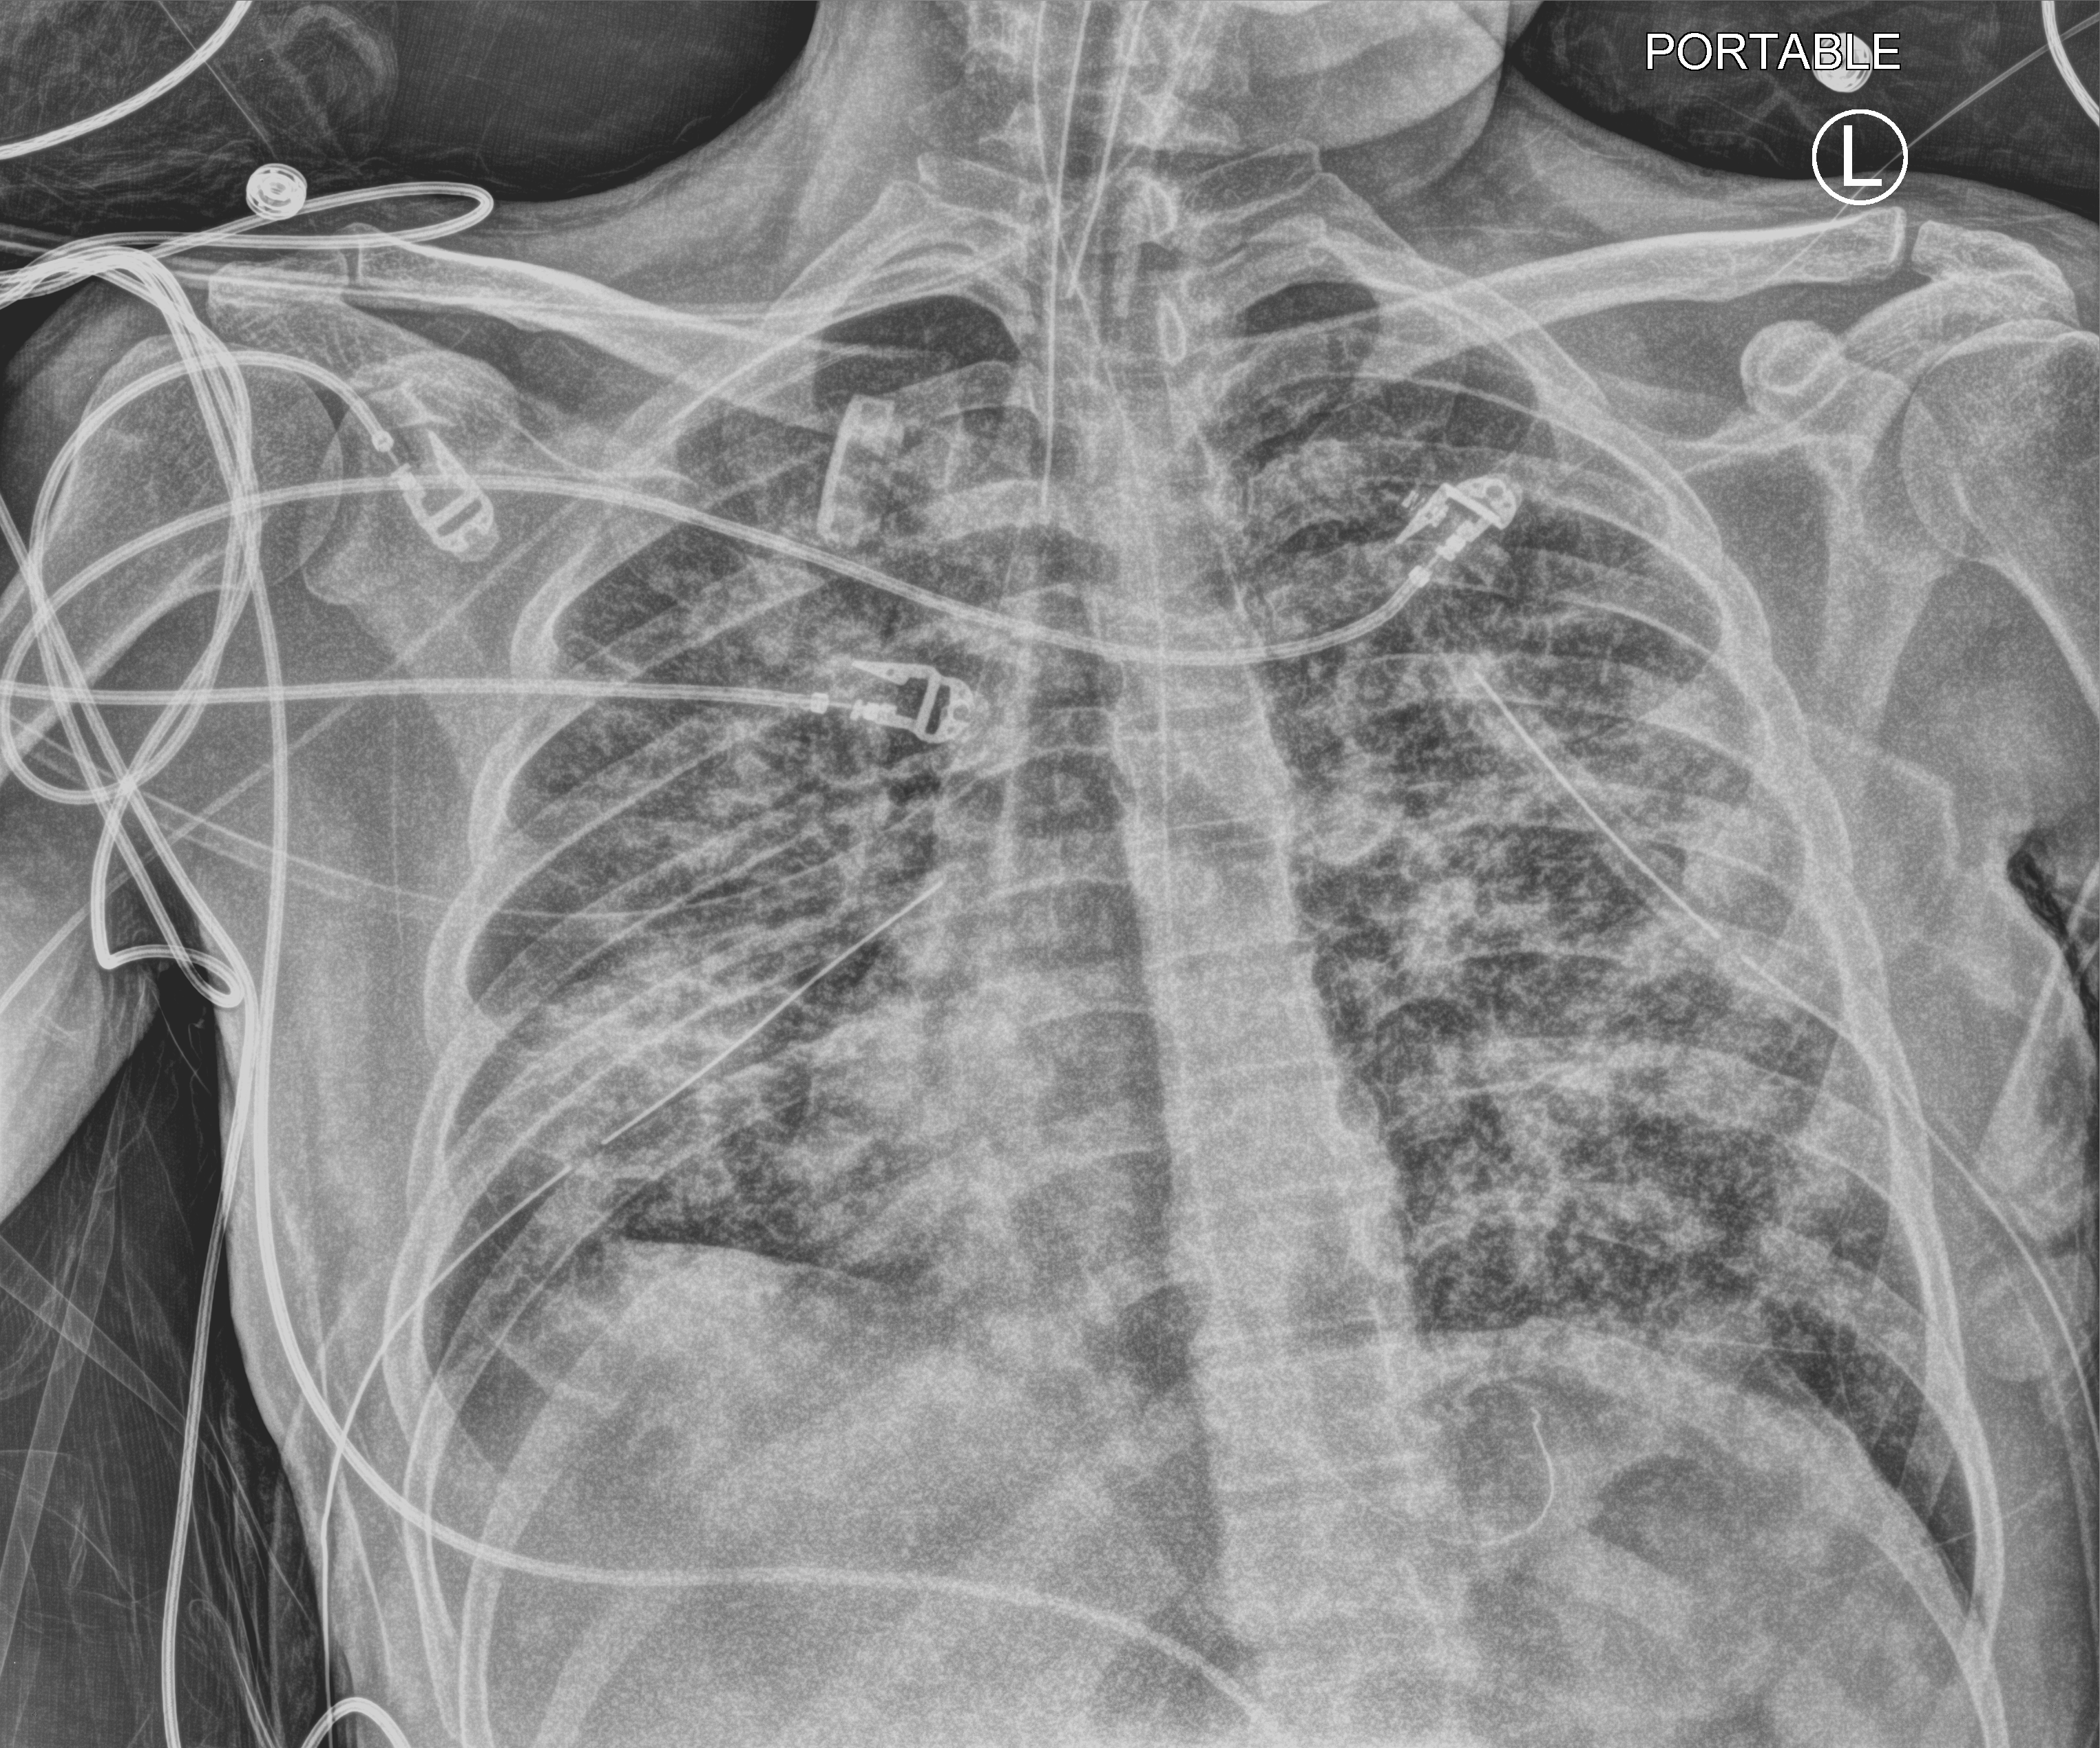
Bedside chest radiograph (computed radiography). Male patient hospitalised with COVID-19, age 18–59 years.
Hospital-stay facts (about this admission, not read from this image; timing relative to this image not recorded): other chronic lung disease (admission record): no; hypertension (admission record): no.